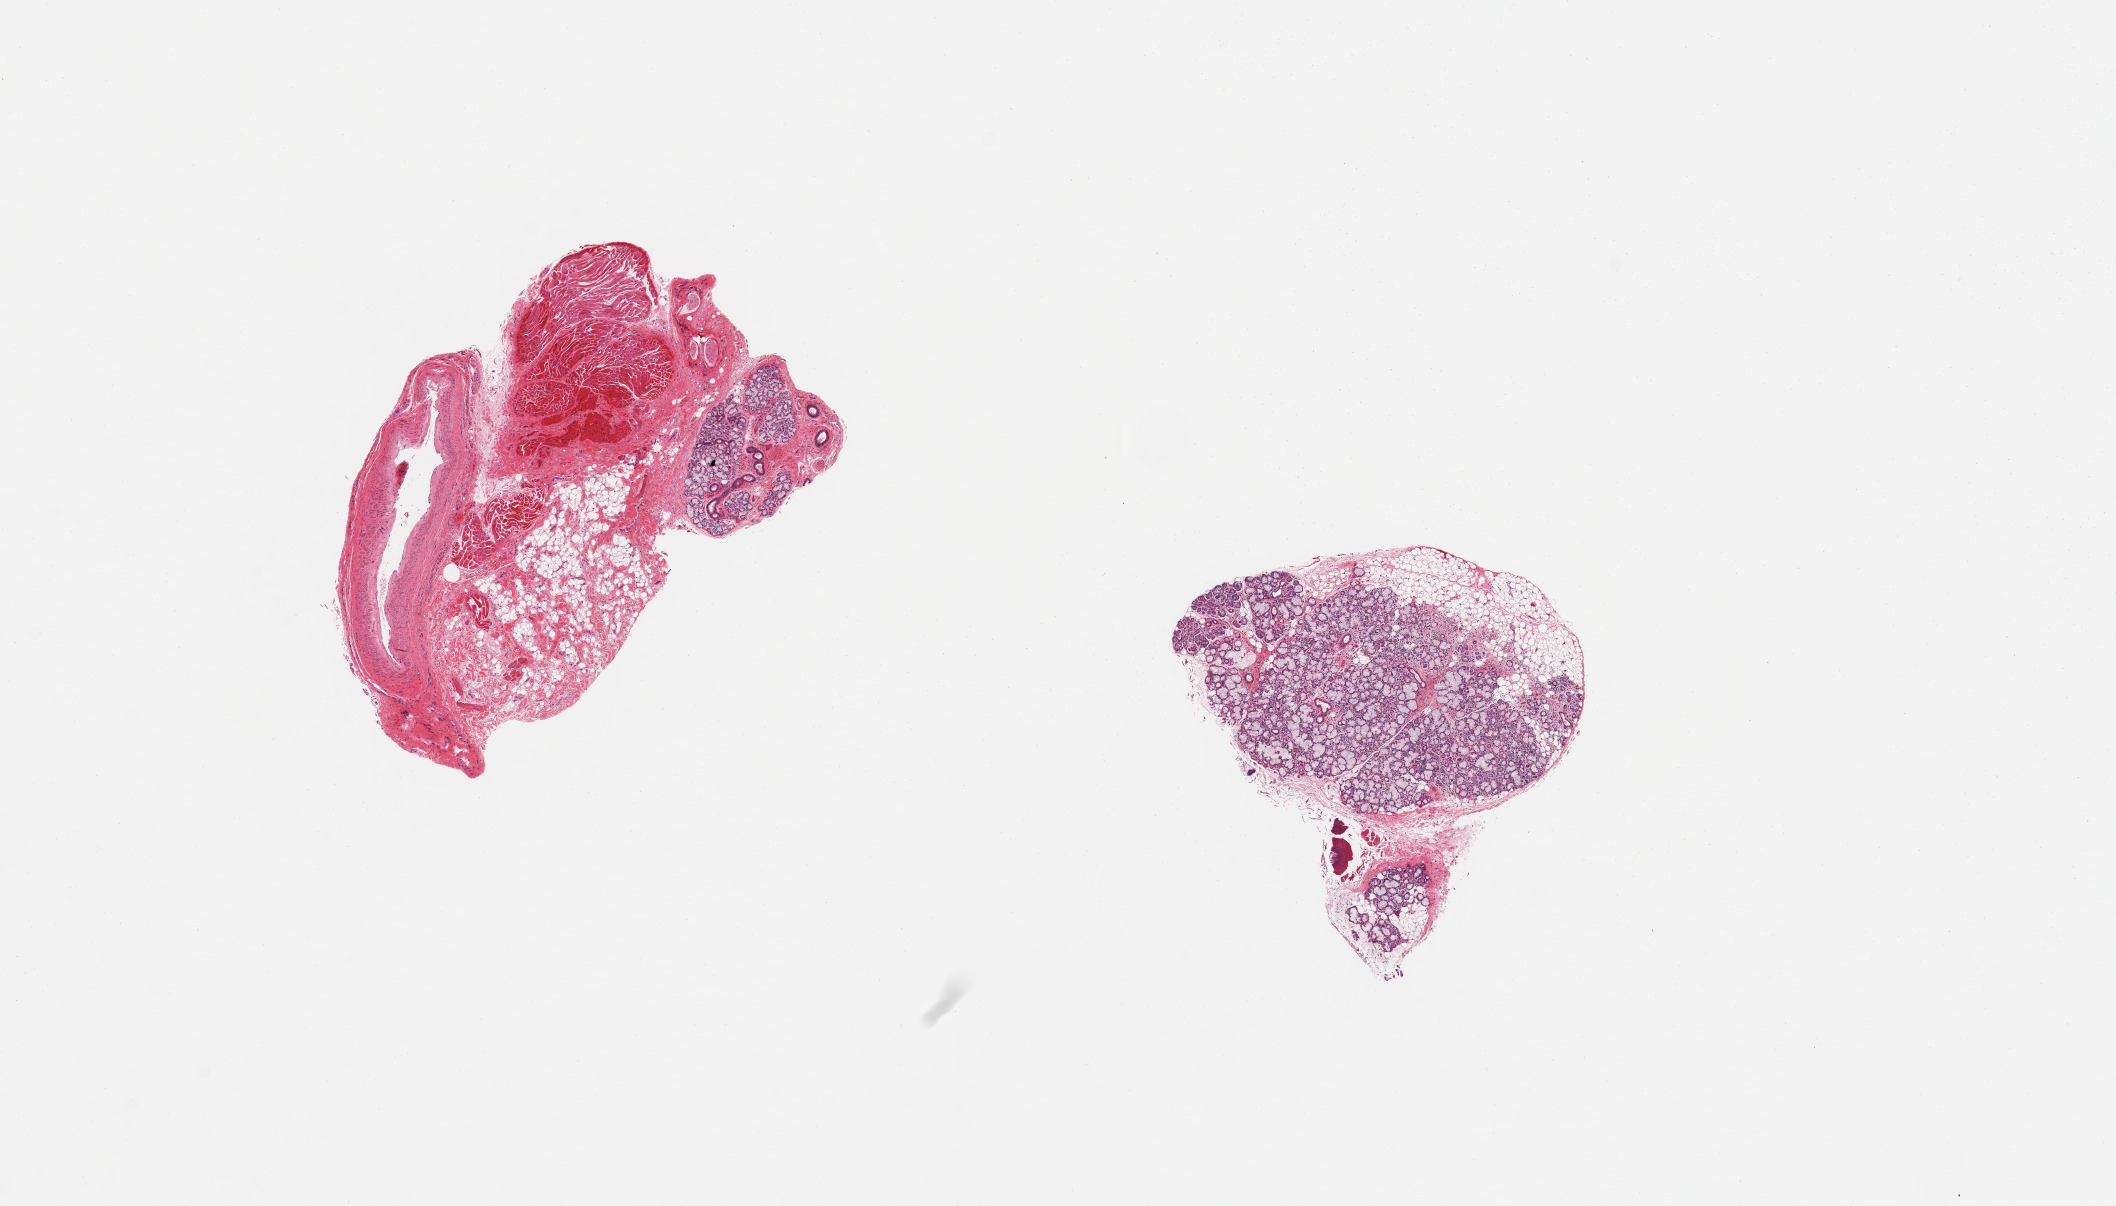
Whole-slide image, H&E stain, brightfield, shown as a low-resolution overview of the whole scanned area (about 16.7 x 9.5 mm, acquisition: 20x scan). PAXgene-fixed paraffin-embedded (PFPE) section. Section of minor salivary gland (target tissue). Donor tissue sample. Donor: male.
* review note (as recorded): 2 pieces; ~50% total tissue is glandular; rest is stroma (one piece is ~90% target, good specimen)